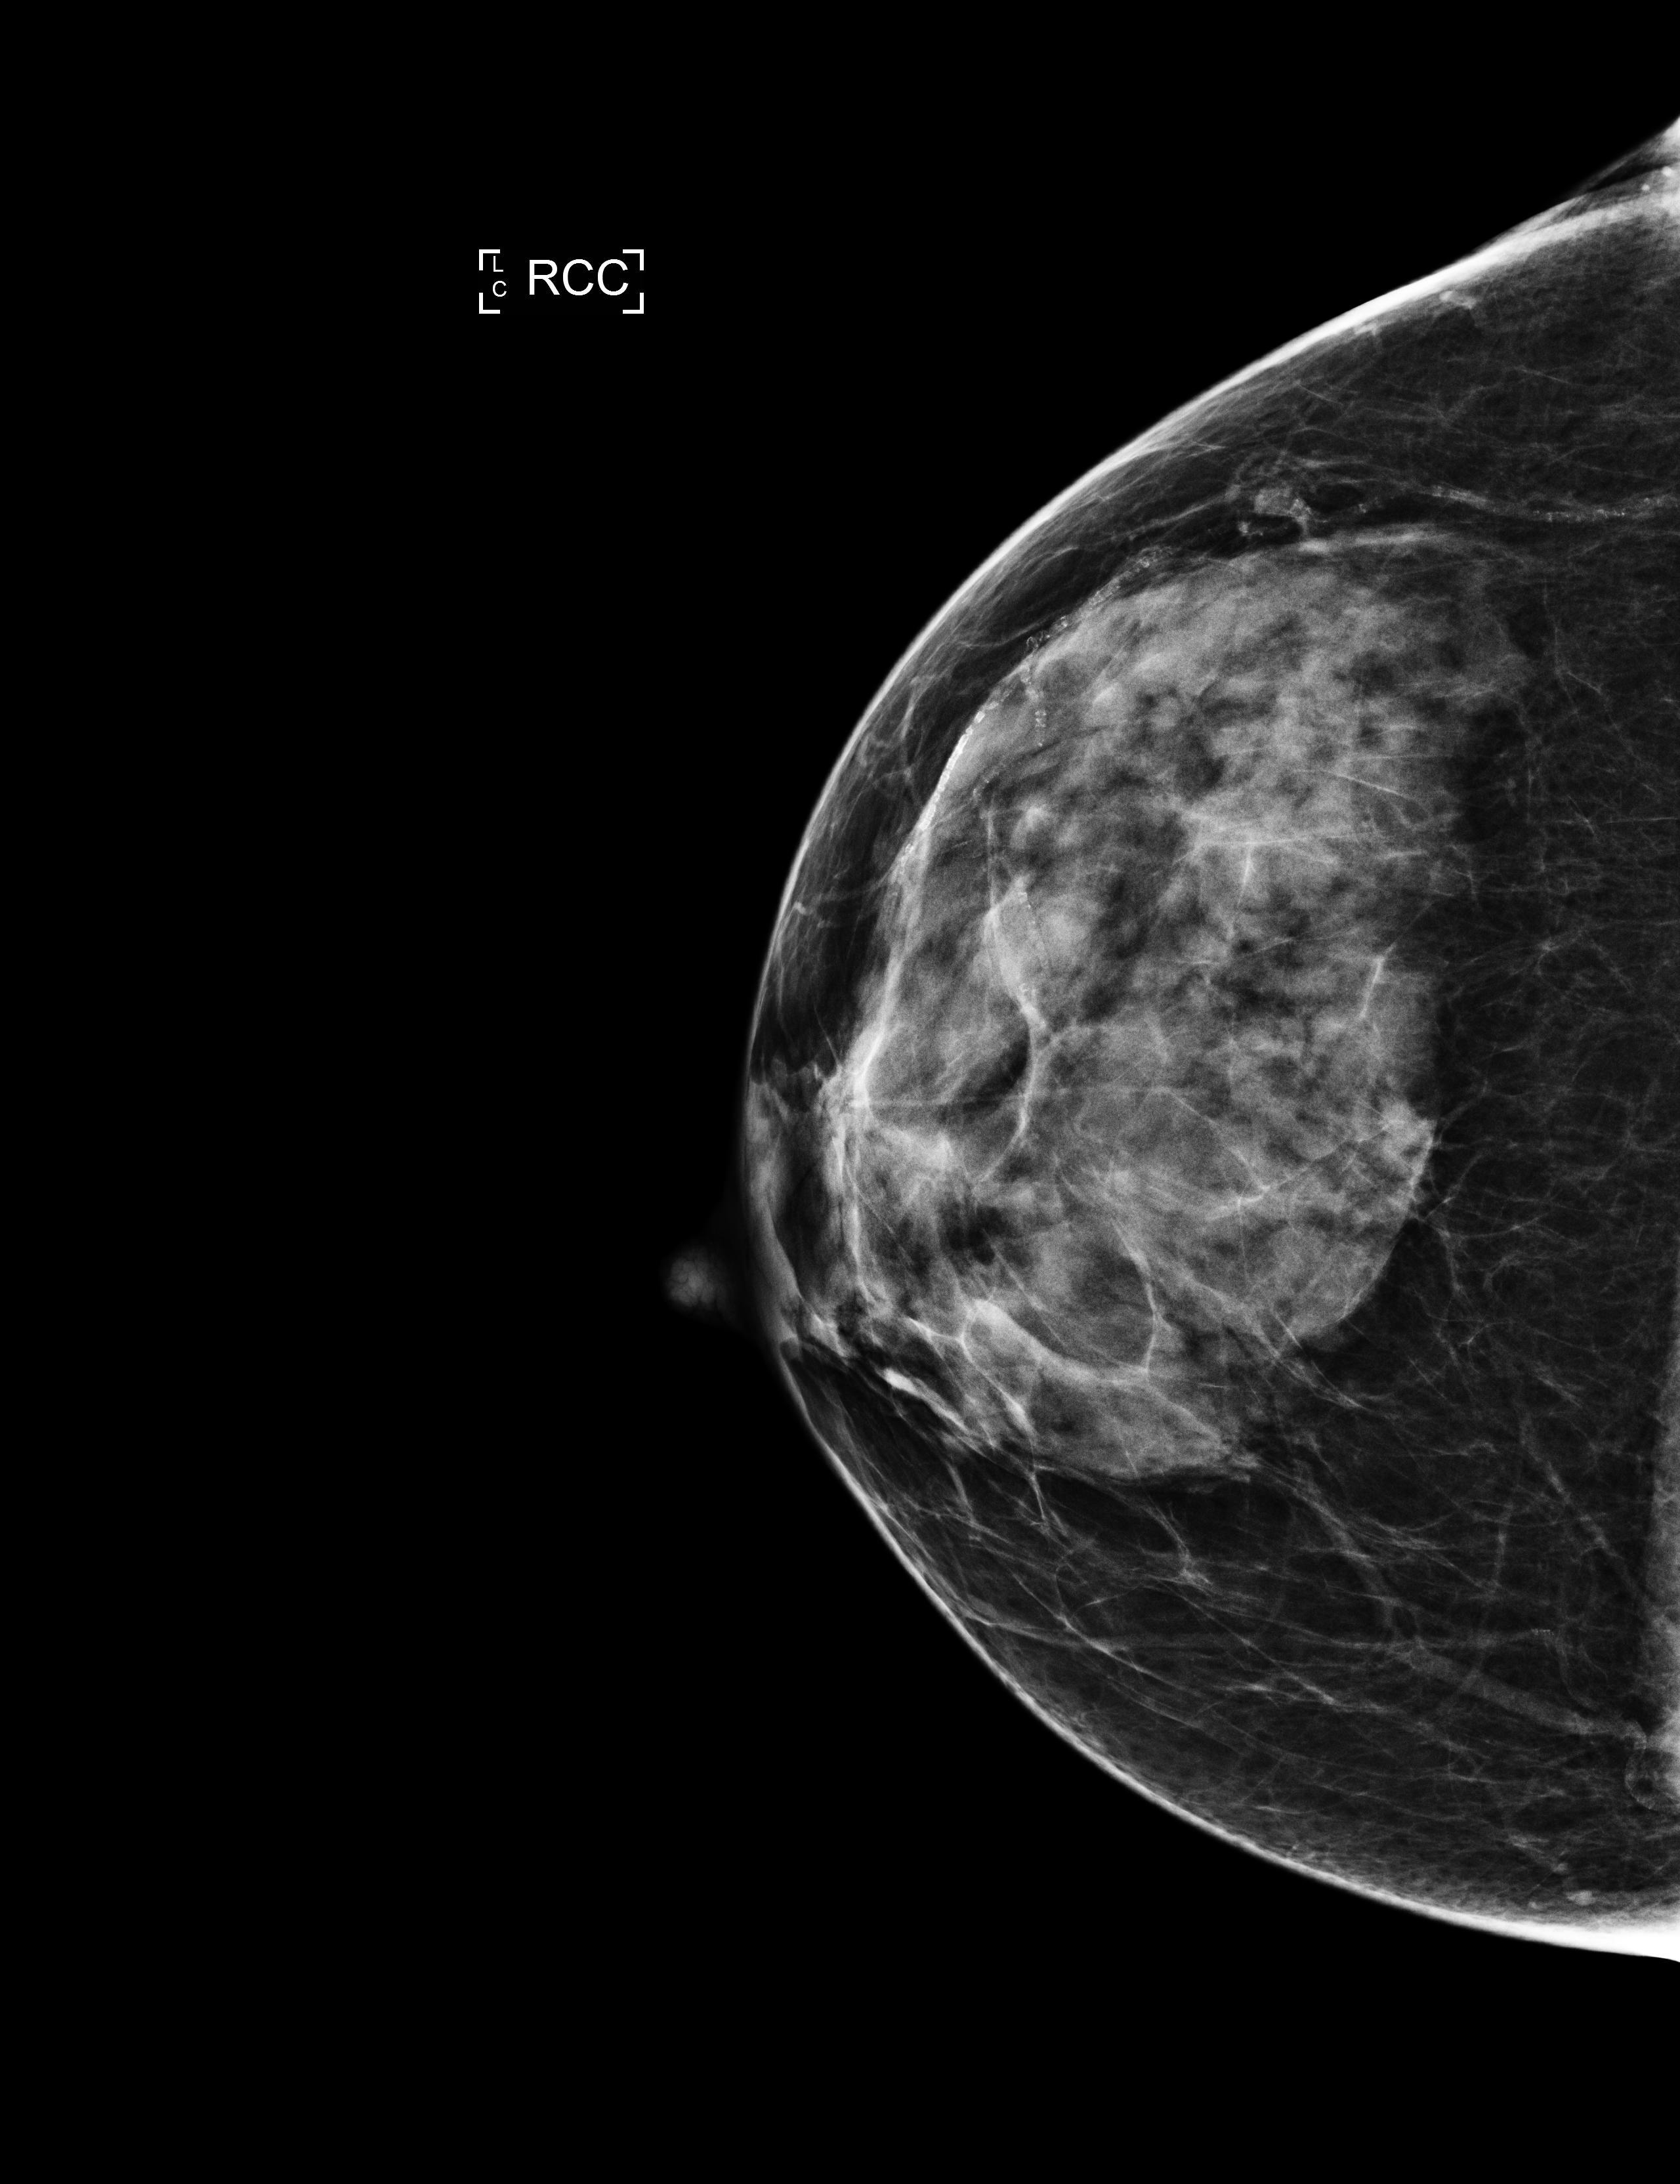
Full-field digital mammogram (FFDM); right breast; craniocaudal (CC) view; annual screening mammography examination; compressed breast thickness 50 mm. Patient: female, 57 years.
BI-RADS breast density category at the screening exam (both breasts, scale 1–4): 3.